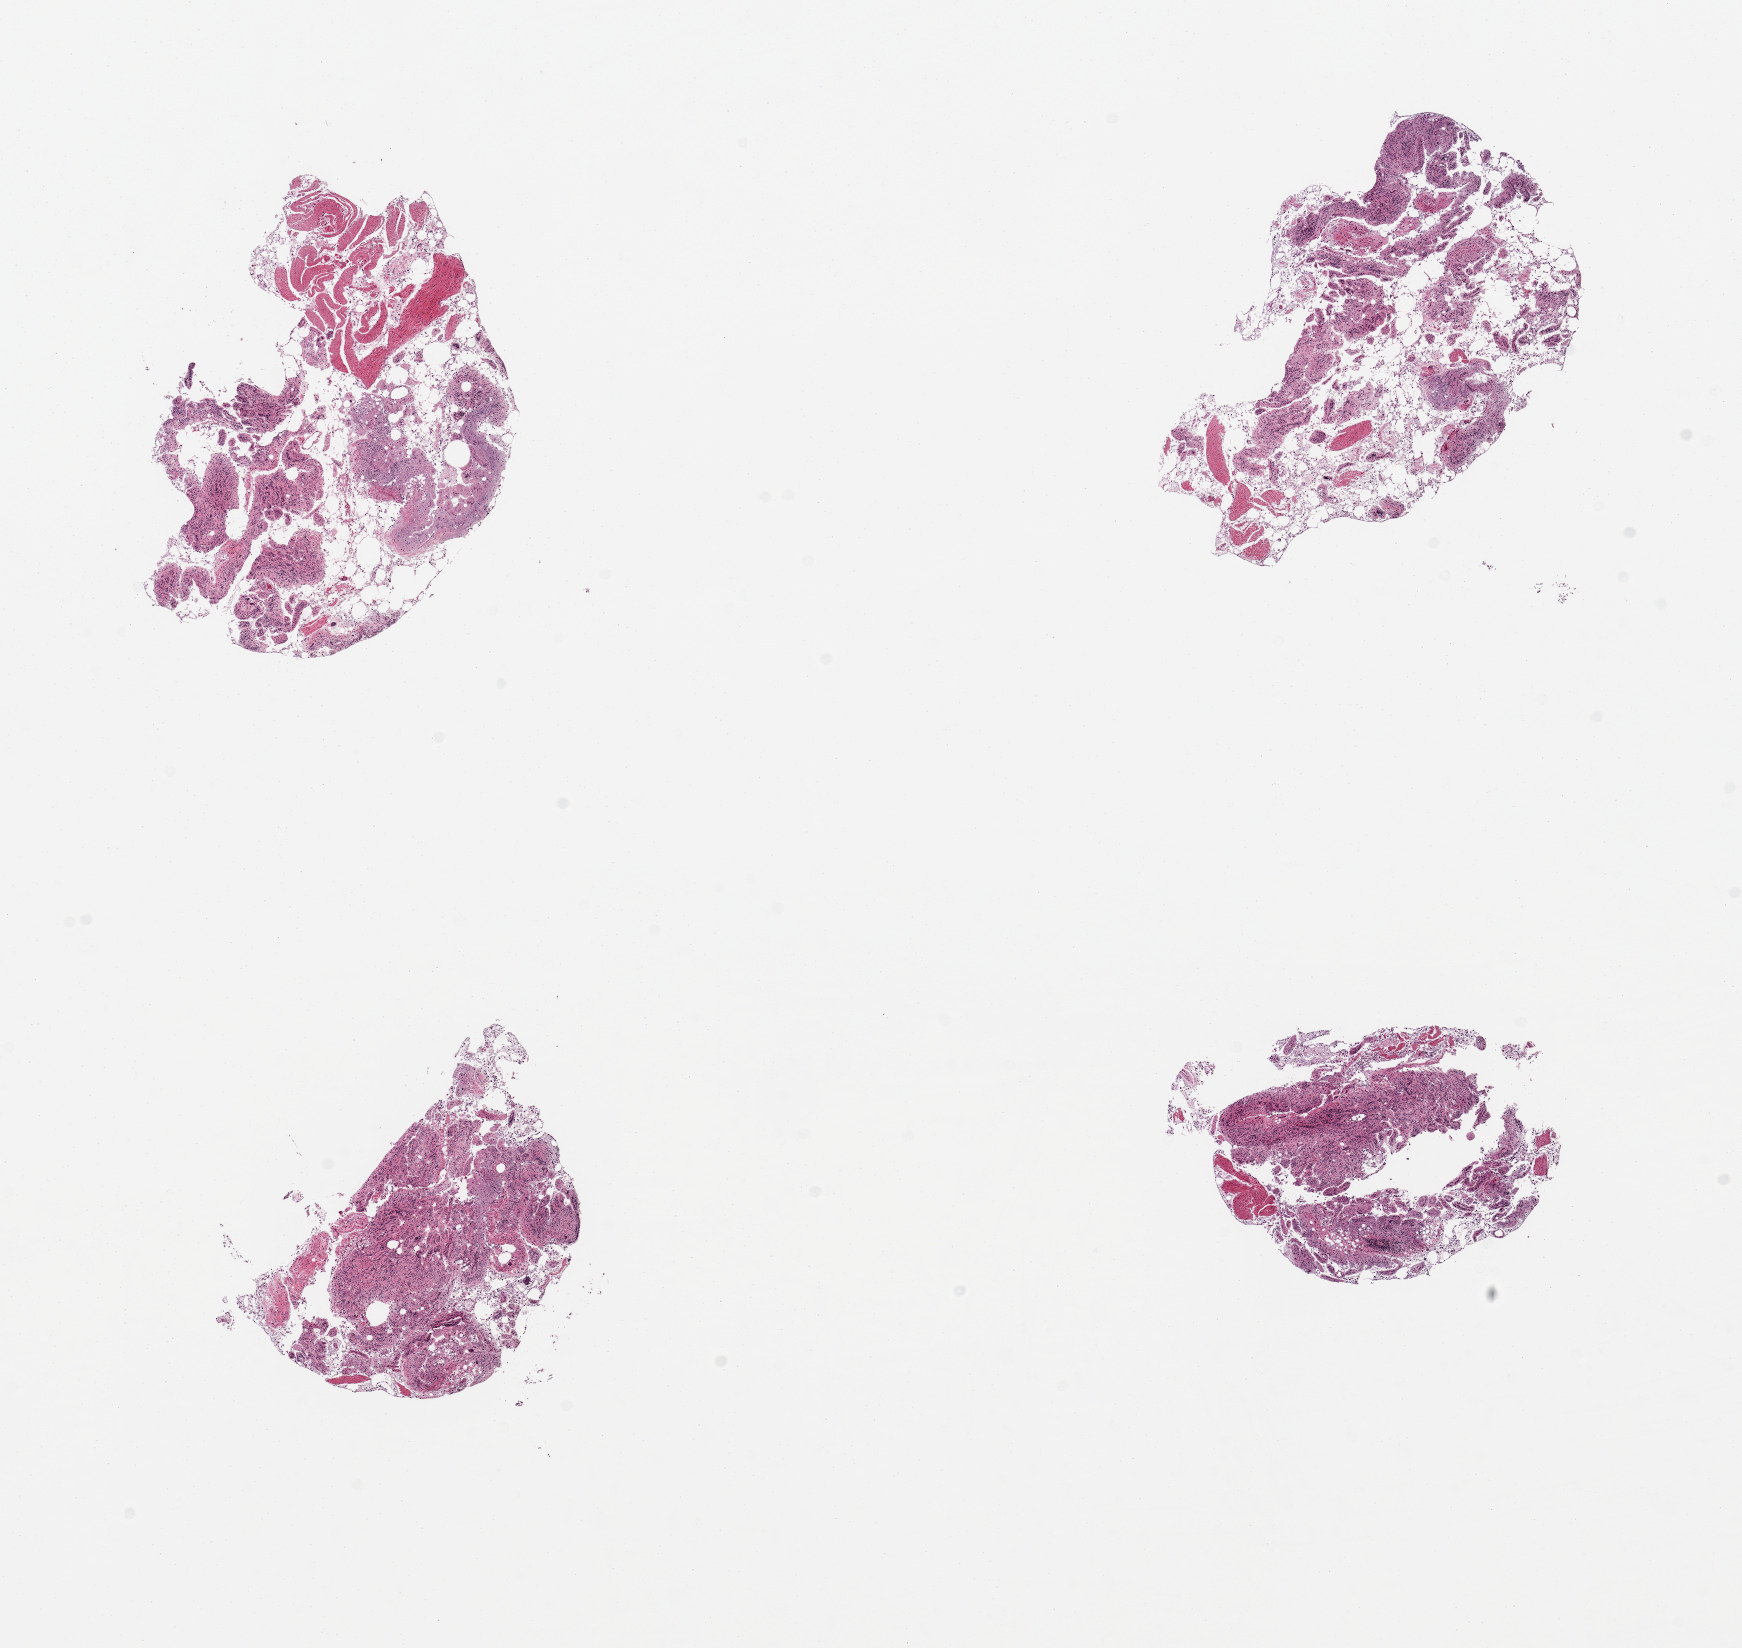
Whole-slide image, haematoxylin and eosin stain, shown as a low-resolution overview of the whole scanned area (about 13.8 x 13.0 mm, slide scanned at 20x). PAXgene-fixed, paraffin-embedded tissue. Target tissue: ileum. Tissue donor sample. Donor: male.
- review note (as recorded): 4 pieces; totally autolyzed mucosa and no evidence of target lymphoid aggregates, fragments of muscularis (not target)